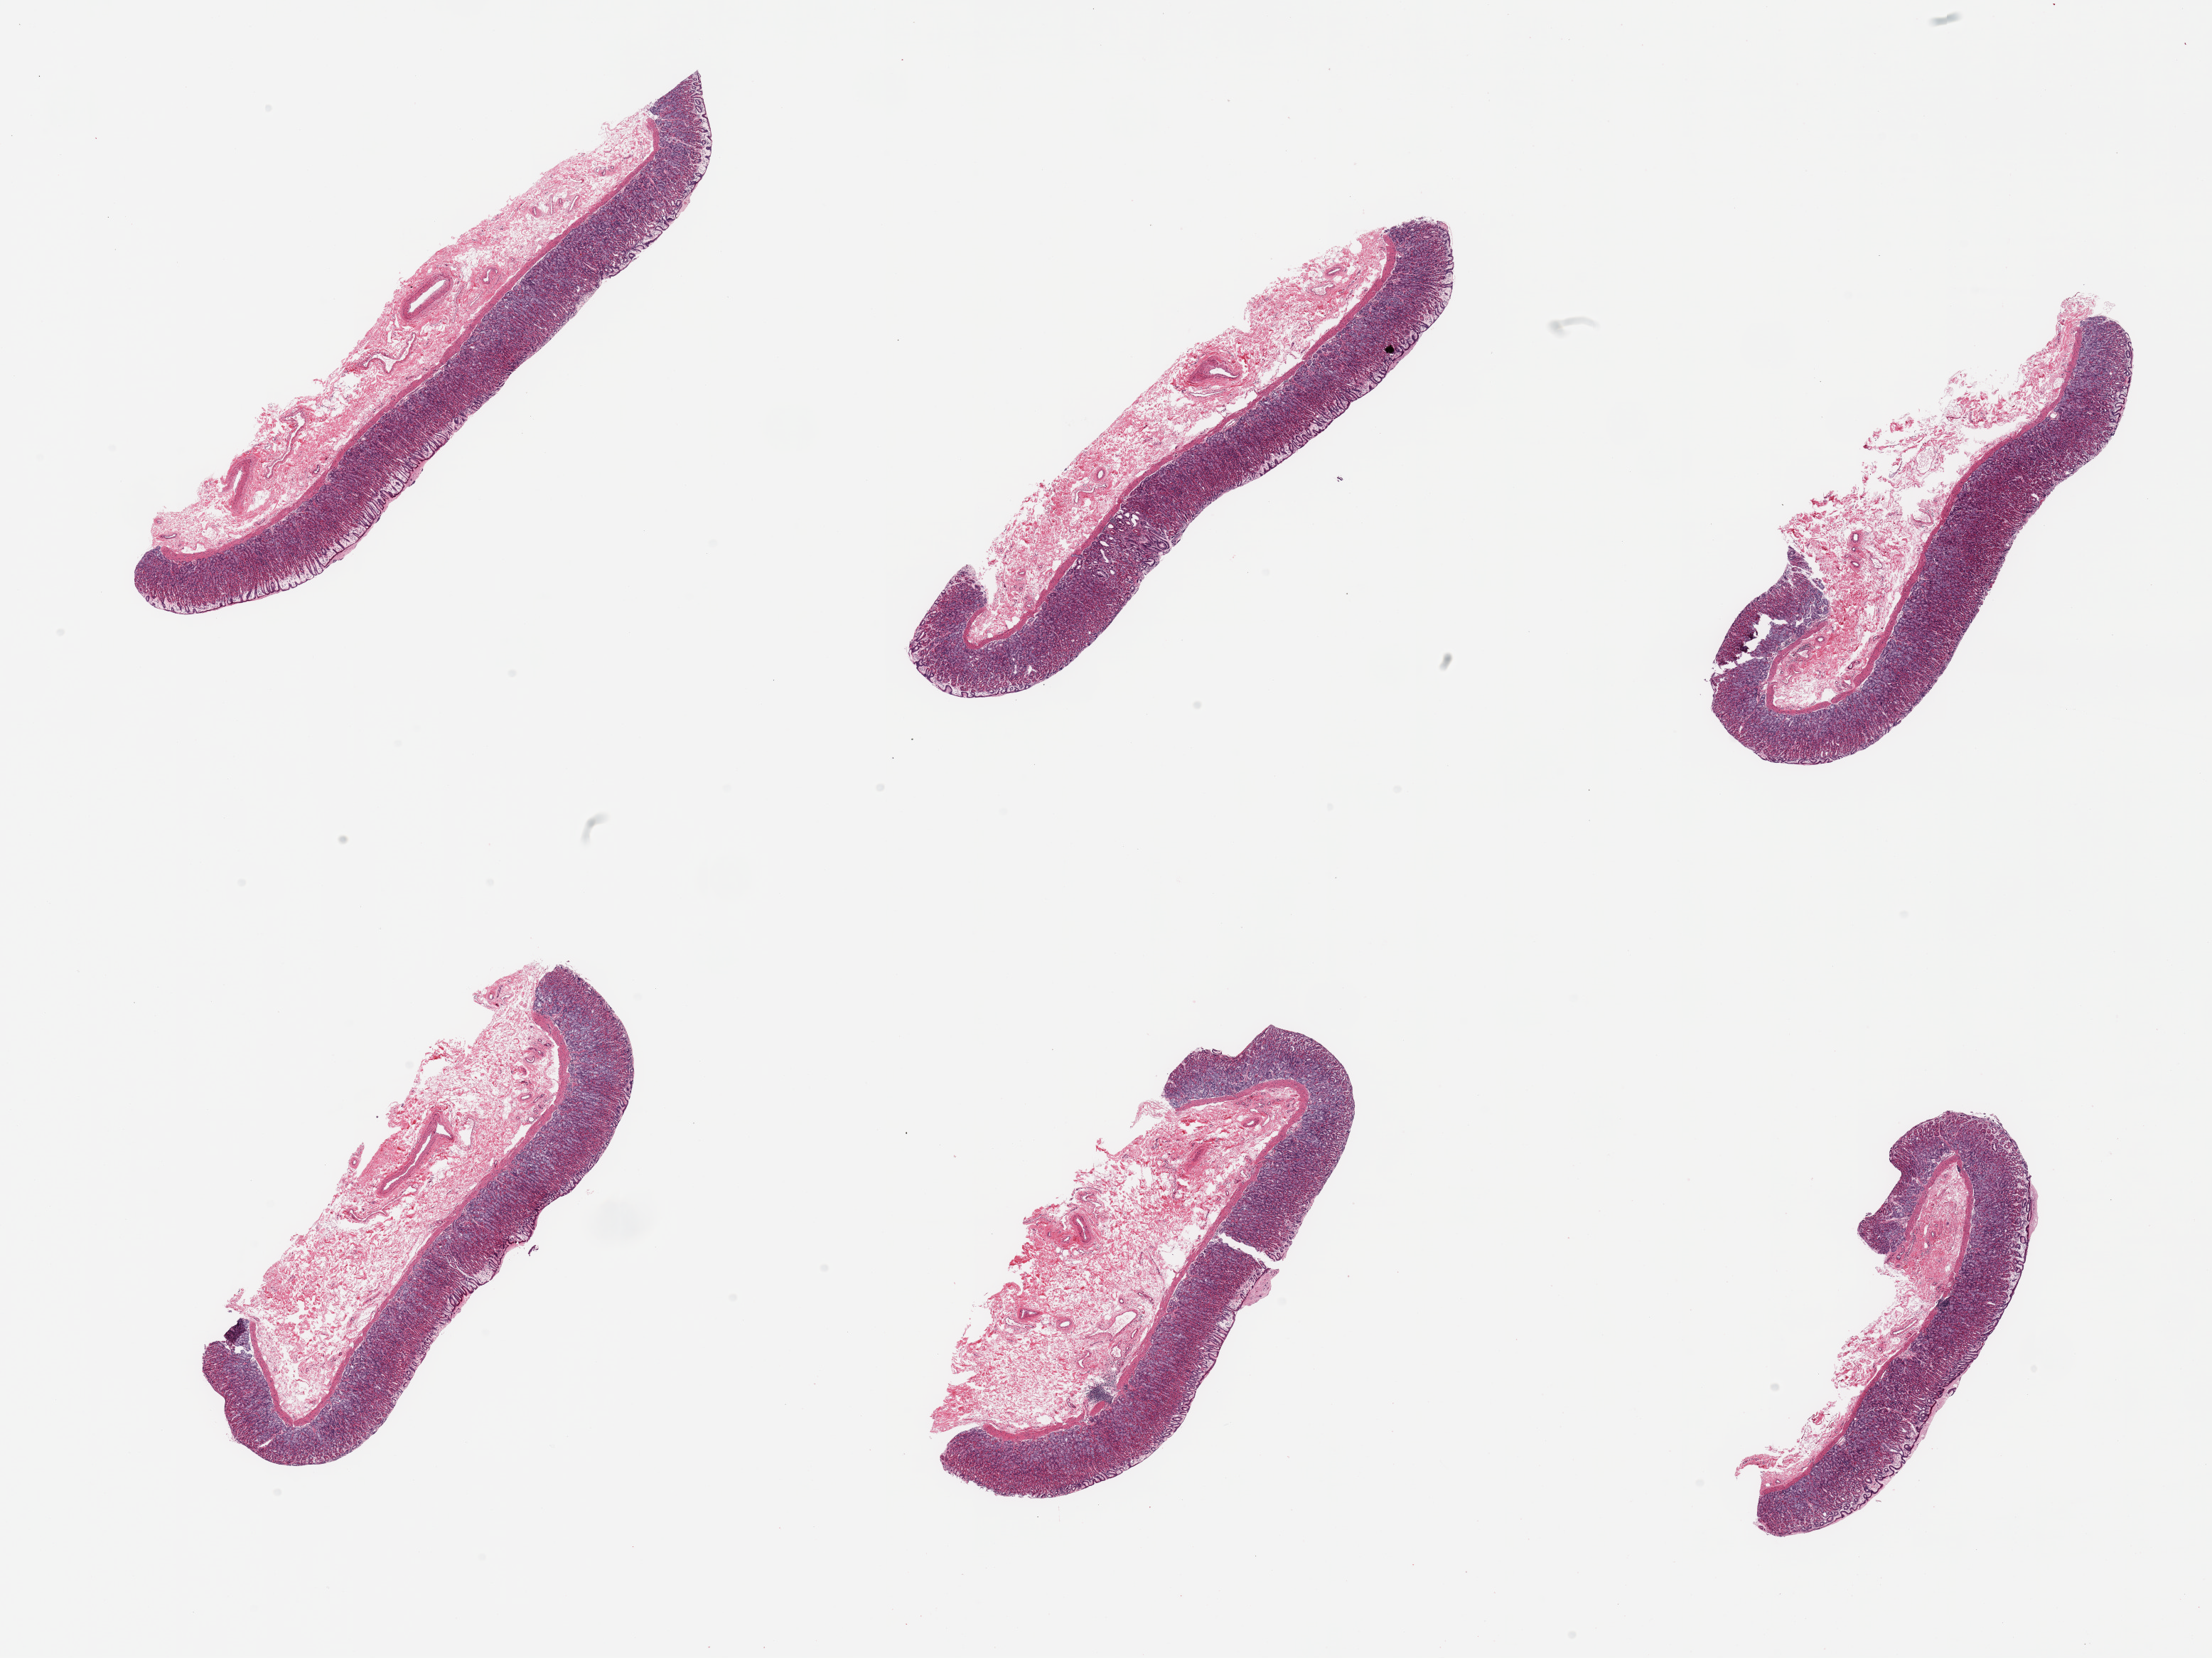
Digitized haematoxylin and eosin-stained section, brightfield, a low-resolution overview of the entire scanned area, about 24.6 x 18.4 mm, PAXgene-fixed, paraffin-embedded tissue, target tissue: stomach, donor tissue sample. Donor sex: female.
Review note (as recorded): 6 pieces; mucosa and submucosa only.